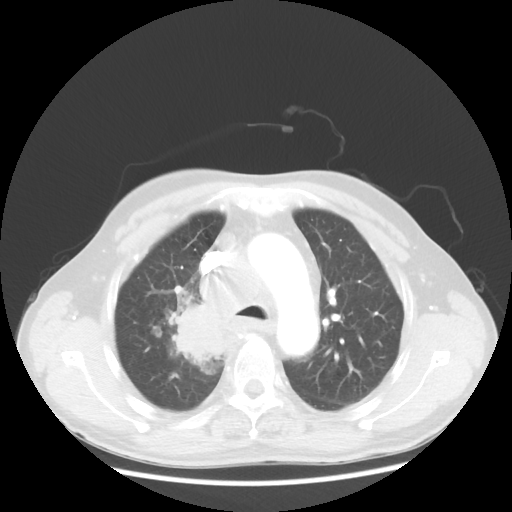
Chest CT, one axial slice; slice 89 of 124 in the series (ordered by position); reconstruction kernel STANDARD; 100 kVp; lung window (W 1500 / L -600 HU); 512 × 512 image matrix. Patient: male, 64 years. From the clinical record (not read from this slice): clinical TNM (as recorded): T3 N3 M0; histopathological grade: G3.
Annotated regions visible in this slice (bounding box drawn by a radiologist):
- lung tumour (recorded histology: small cell carcinoma): bounding box [x1, y1, x2, y2] px = [160, 295, 239, 375]